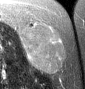
MRI of an extremity soft-tissue mass, one axial slice. Position 21 of 46 along the scan axis. T2-weighted fat-saturated. MR volume resampled by the dataset authors to the PET/CT grid (not the native acquisition matrix). 3.27 mm slice thickness. 85 × 89 image matrix, field of view 83 × 87 mm. Female patient. Case-level facts recorded for this patient, not image findings: histological type: leiomyosarcoma; grade: intermediate; site of the primary tumour: parascapusular.
Structures marked on this image (expert contour drawn on MRI and transferred to this co-registered scan by the dataset authors):
- gross tumour volume including surrounding oedema: bounding box <20,23,67,72> (left, top, right, bottom; pixels)
- gross tumour volume (mass): <20,23,67,72>